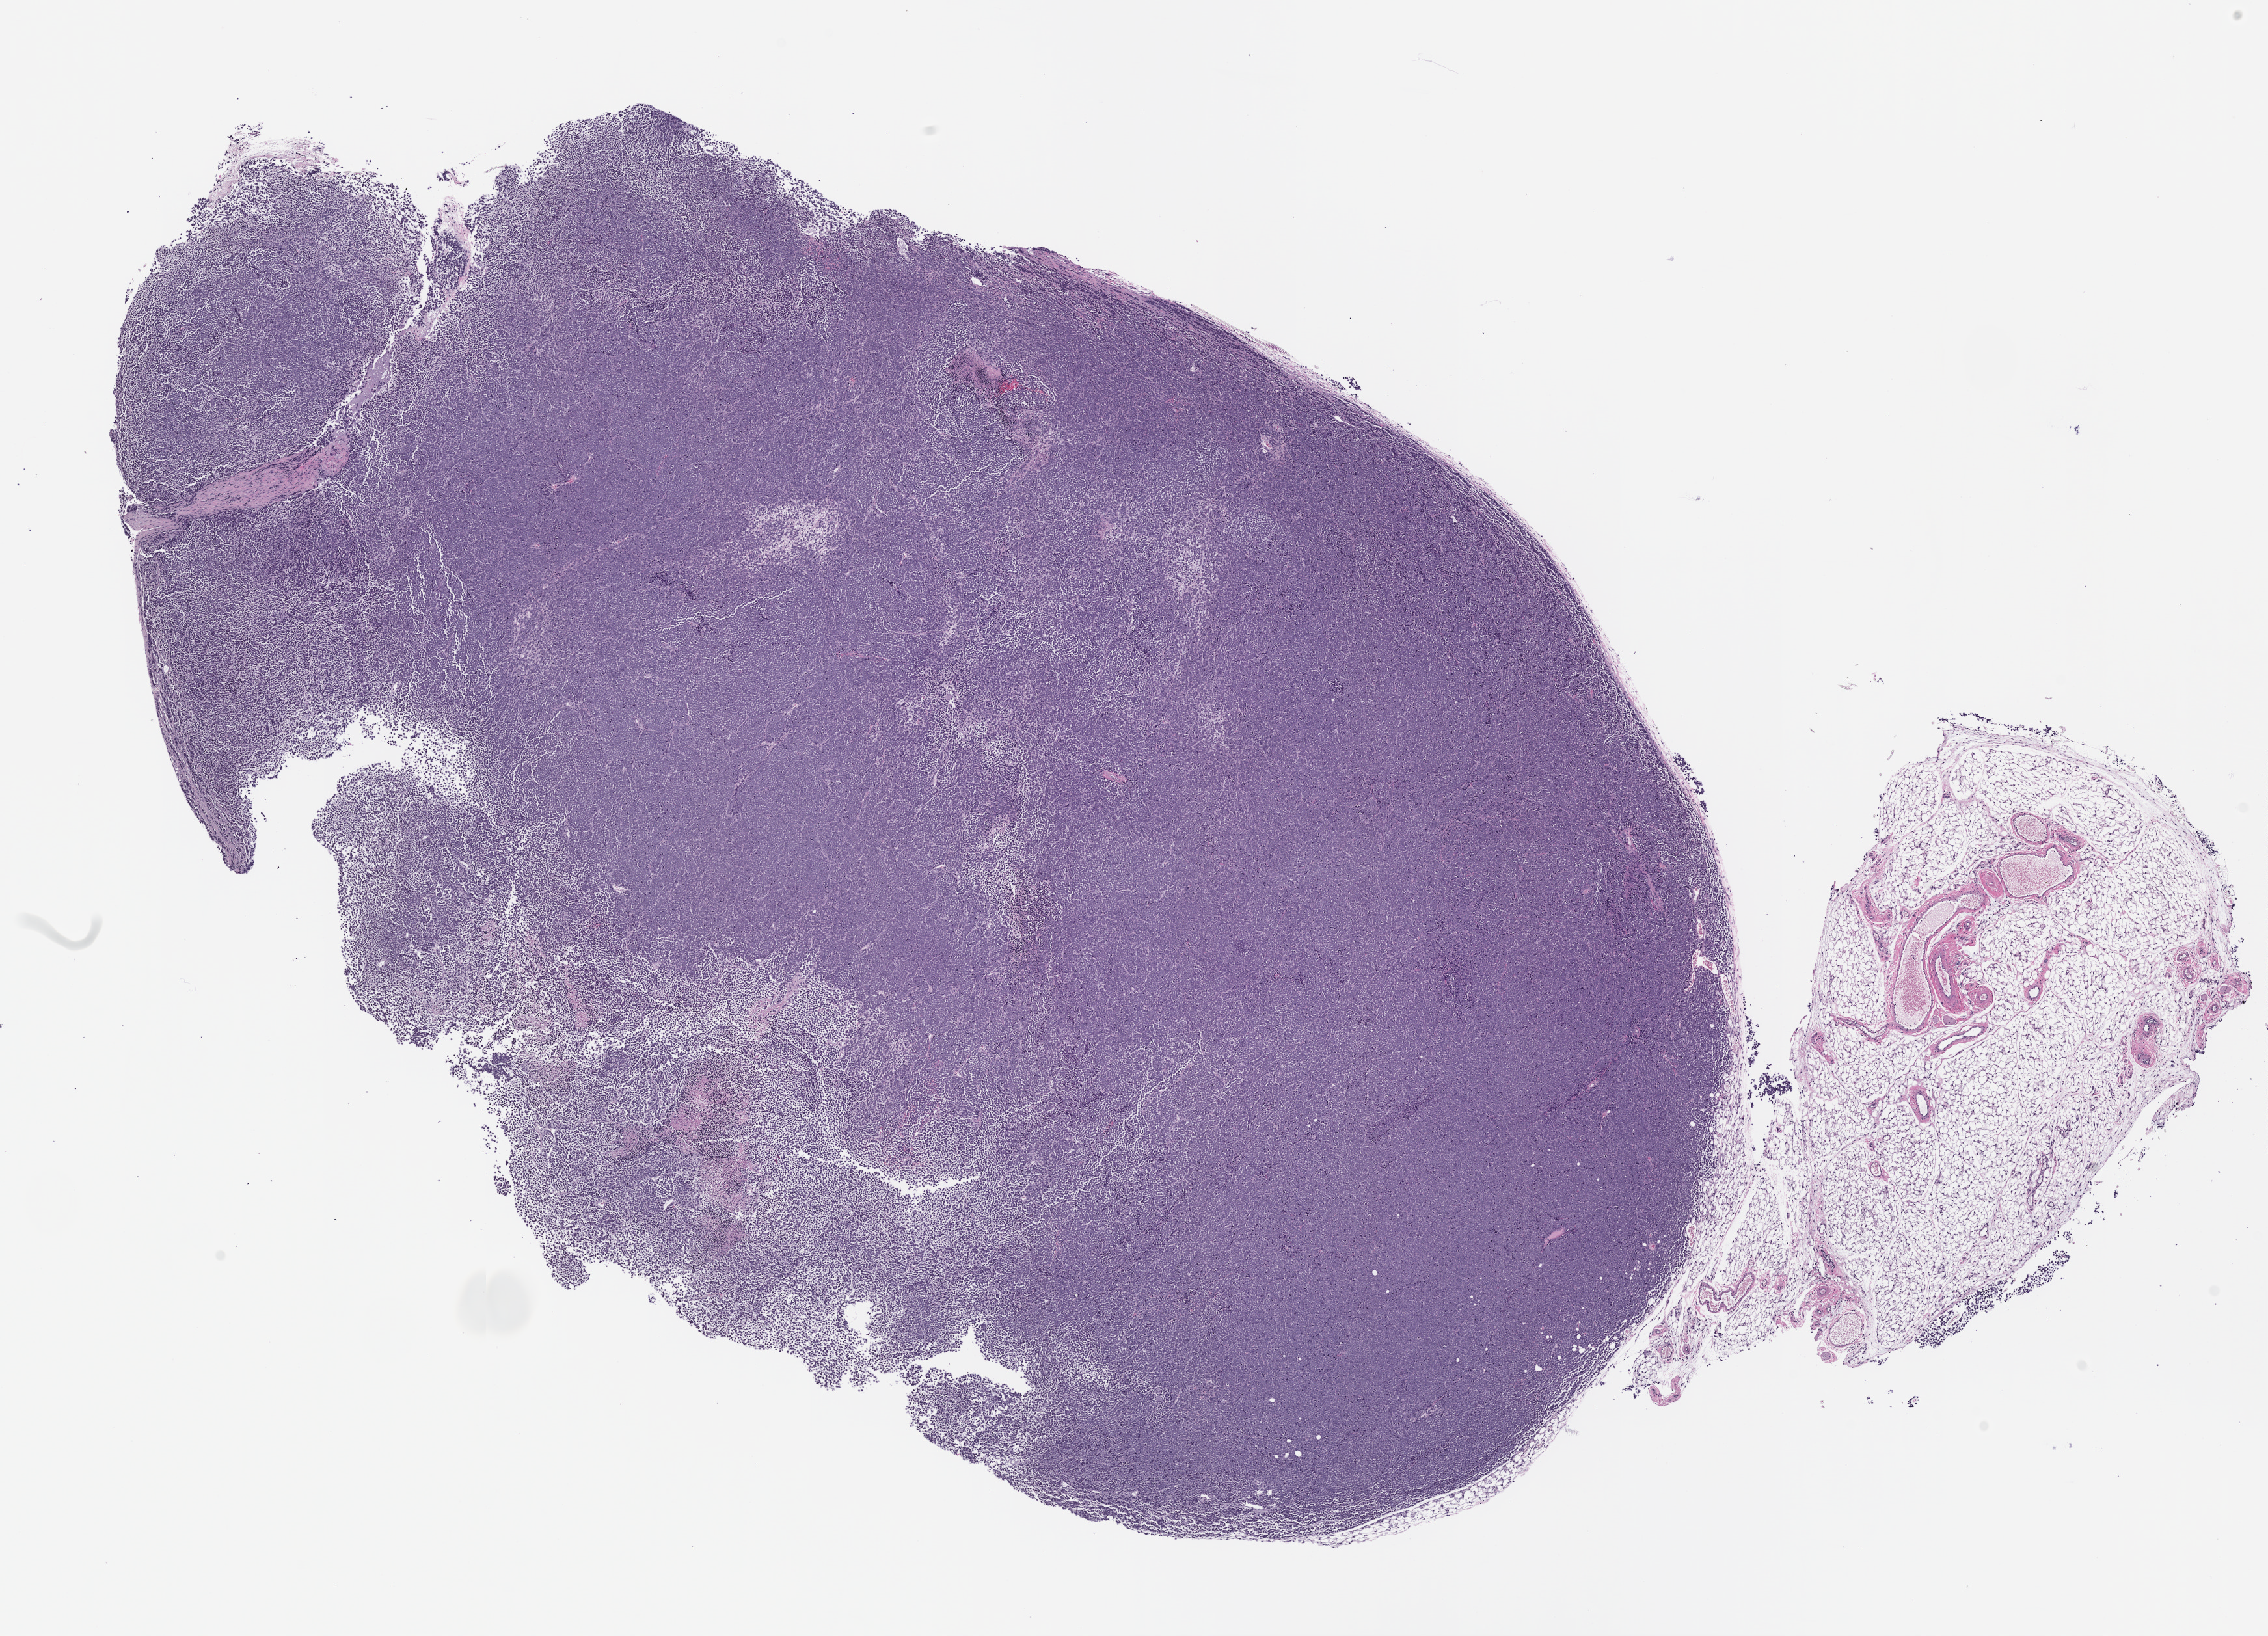
Whole-slide image, H&E: patient-derived xenograft (human tumor grown in a mouse), passage 1 — whole scanned area (about 14.0 x 10.1 mm) shown as a low-resolution overview; formalin-fixed, paraffin-embedded (FFPE) tissue; tumor site category: endocrine.
Originating patient diagnosis: Merkel Cell Carcinoma.